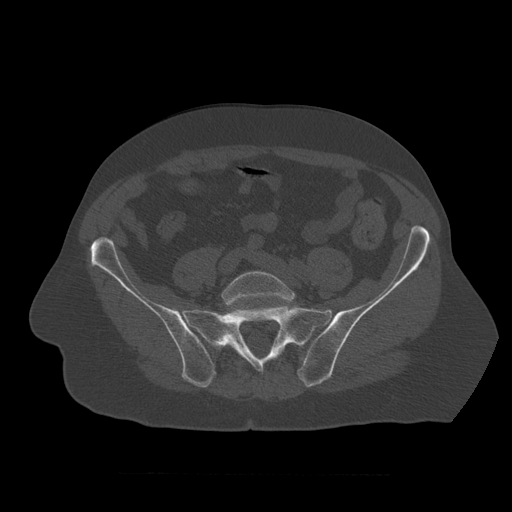
CT including the spine, one axial slice. Position 241 of 450 along the scan axis. Reconstruction kernel STANDARD. 120 kVp. Bone window (W 1800 / L 400 HU). 1.25 mm slice thickness. 512 × 512 image matrix. Patient age 75 years. From the clinical record (not read from this slice): primary cancer: prostate.
Annotated regions visible in this slice (semi-automatic segmentation, software-assisted and operator-edited):
- L5 vertebra: bounding box <222,271,296,307> (left, top, right, bottom; pixels)